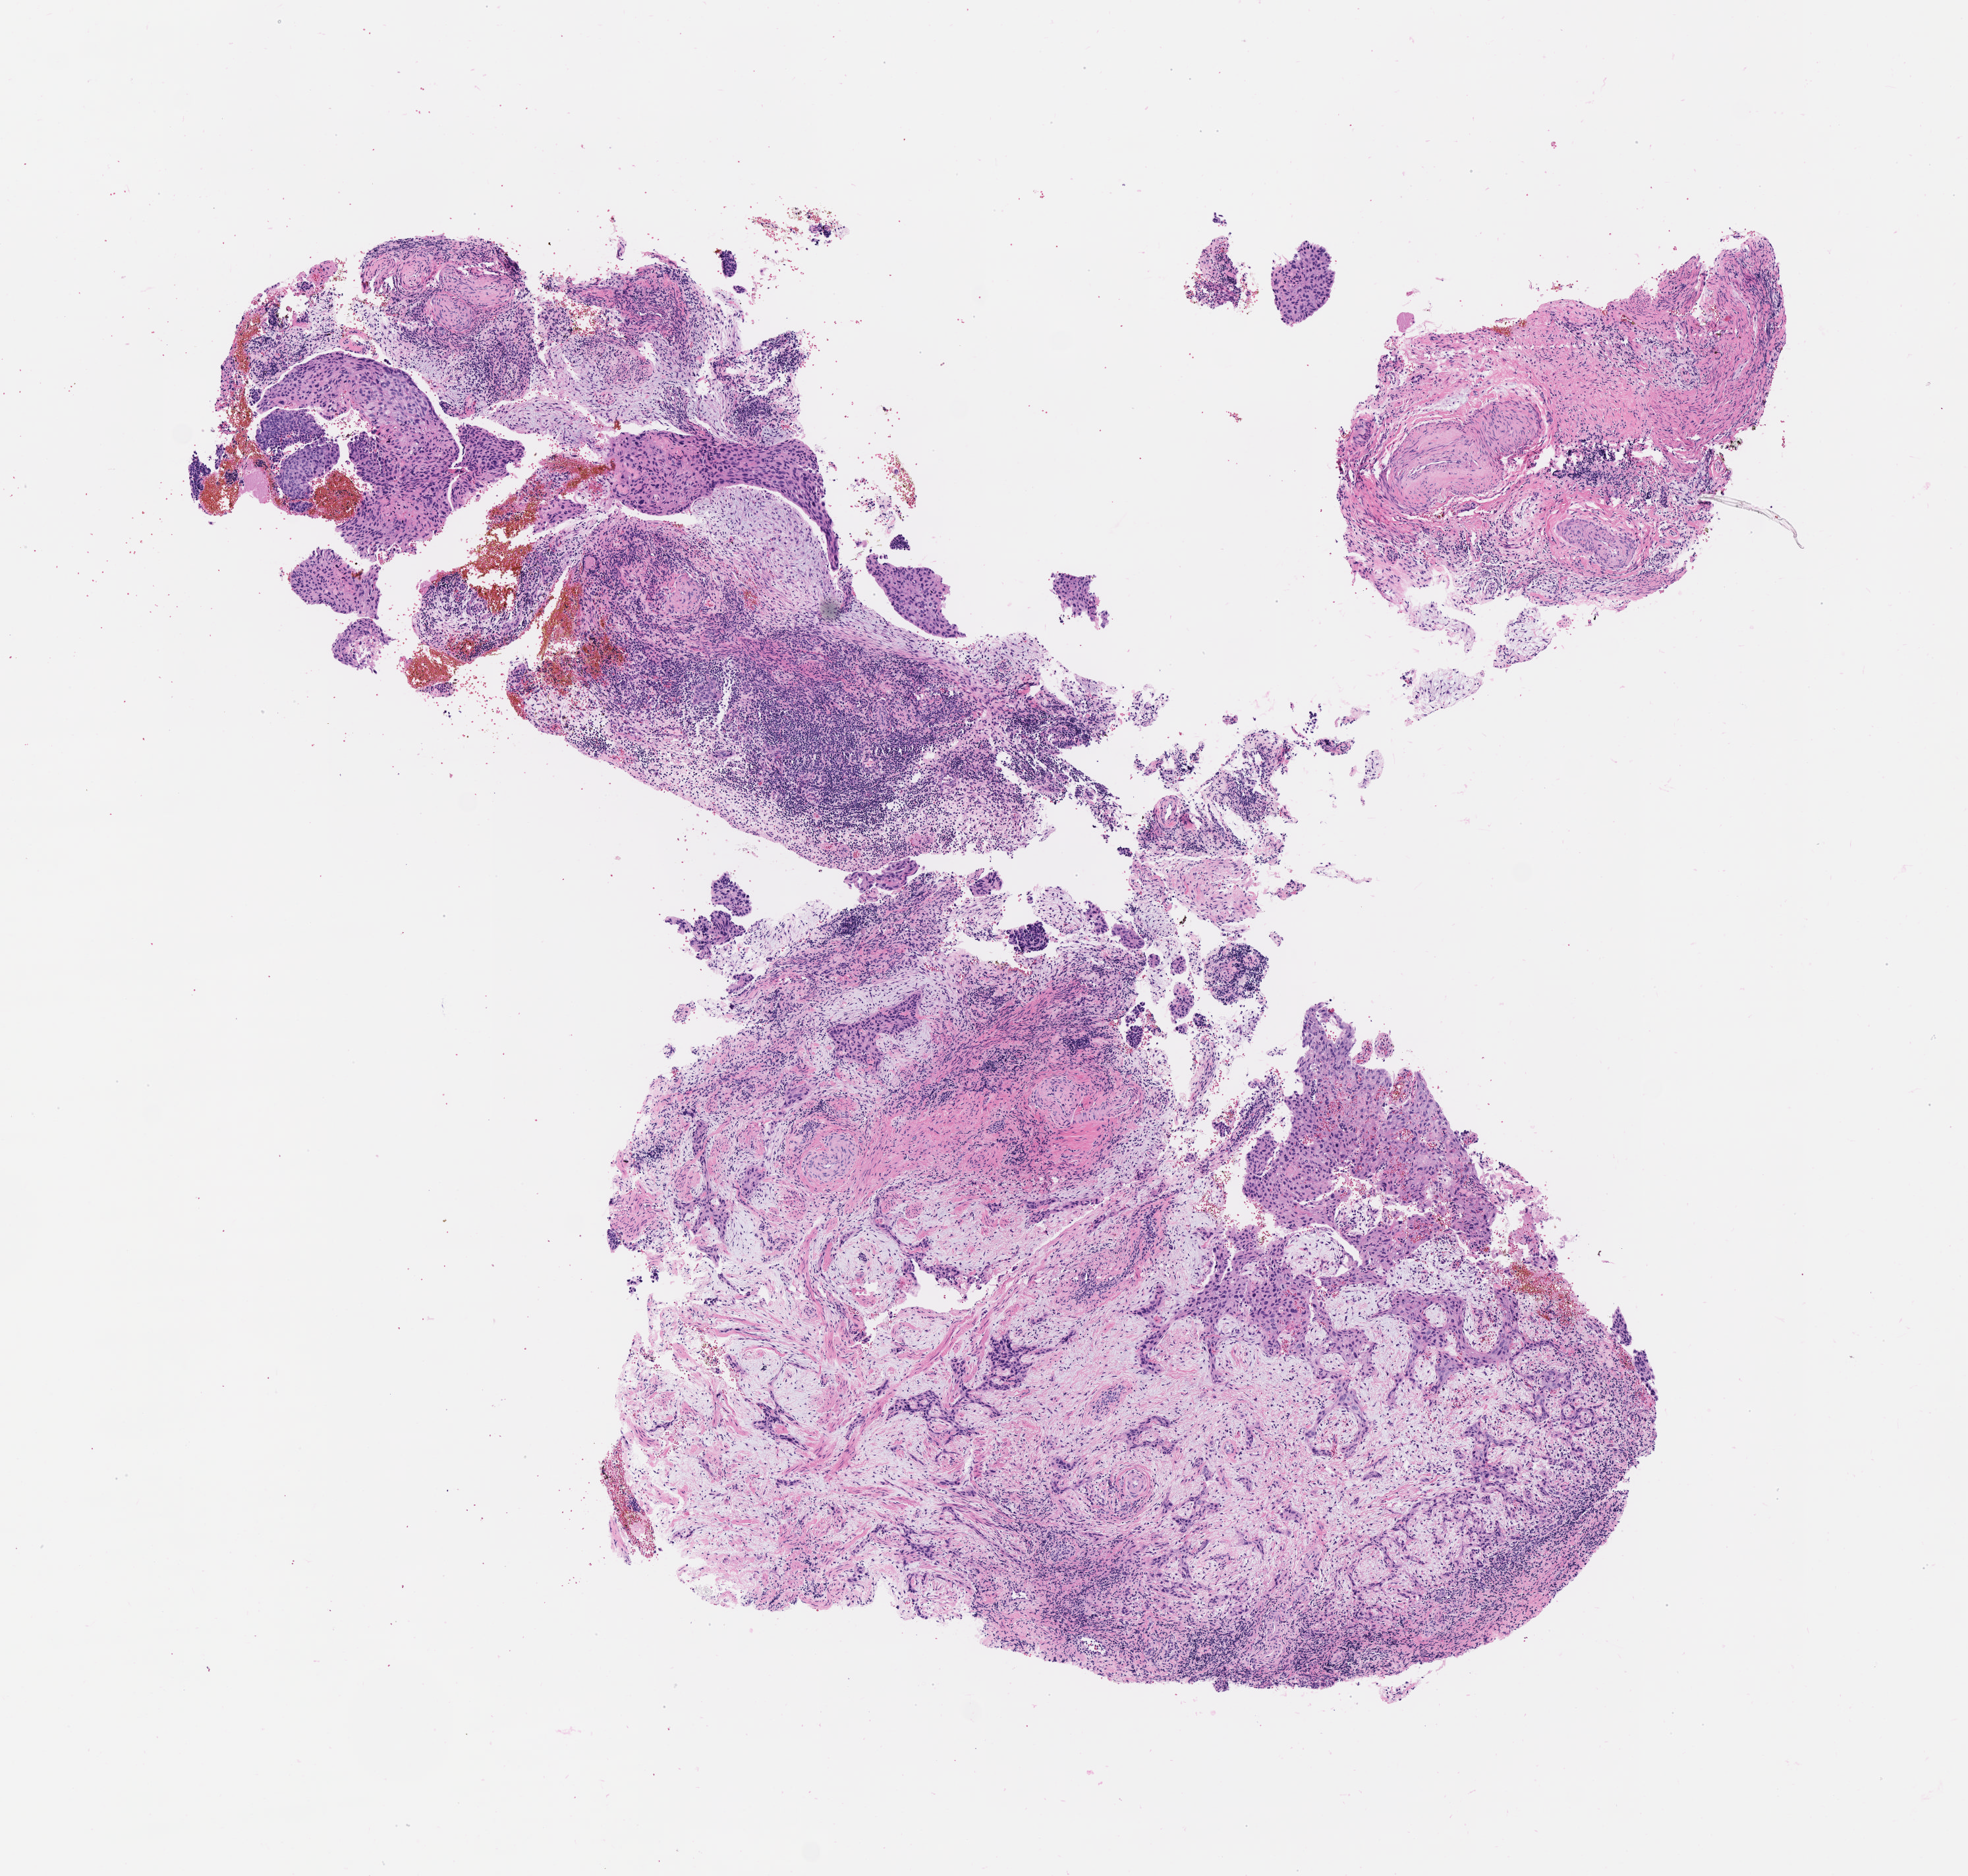
H&E whole-slide image, low-resolution overview of the scanned area, about 6.0 x 5.8 mm; tumor tissue; anatomic site: cervix. Patient female; aged 57.
* histologic diagnosis: Squamous cell carcinoma, large cell, nonkeratinizing, NOS